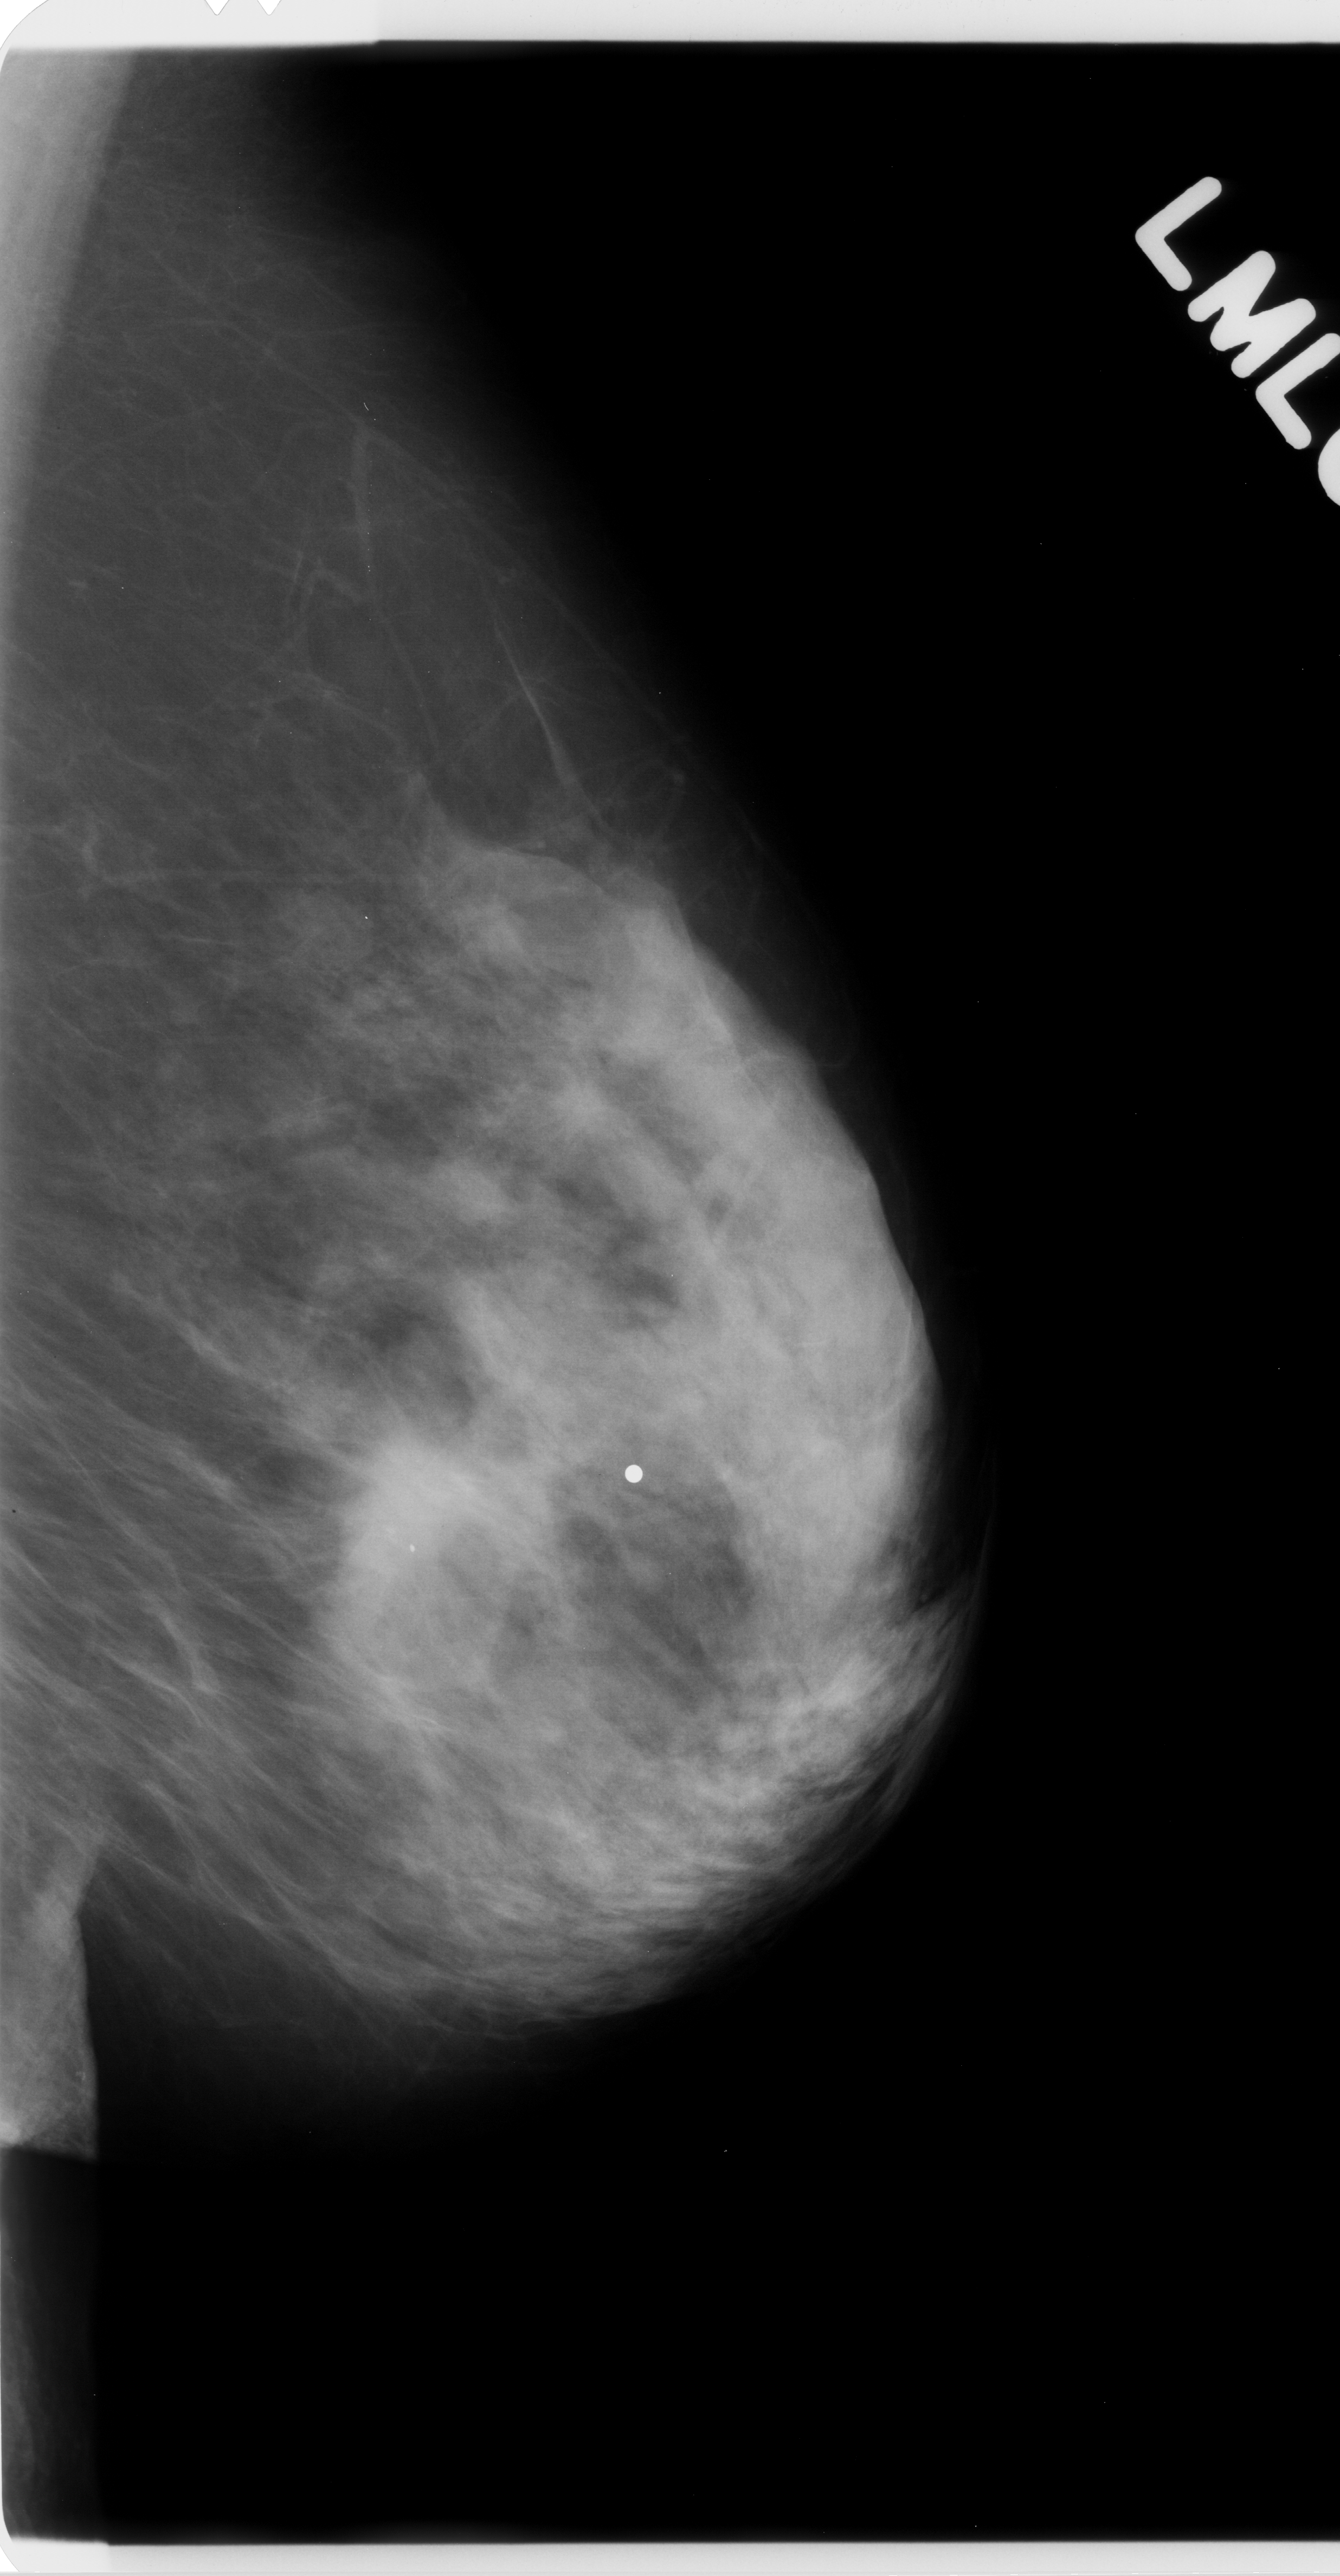
Scanned film-screen mammogram. Left breast. MLO view. BI-RADS breast density category 3 (scale 1–4). 1340 × 2576 image matrix.
Expert-marked regions of interest on this film, with their recorded descriptors:
- mass, shape round, margins spiculated; BI-RADS assessment category 5; subtlety rating 5 on a 1 (subtle) to 5 (obvious) scale; pathology result (as recorded, not read from the image): malignant: bounding box (x1, y1, x2, y2) in pixels: (356, 1411, 529, 1558)